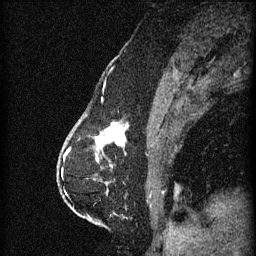
Breast MRI (dynamic contrast-enhanced), one sagittal slice; slice 23 of 60 in the series (ordered by position); 3 images stored at this slice position (order not interpretable as contrast timing); 1.5 T; TE 4.2 ms, TR 11 ms; 256 × 256 image matrix, field of view 180 × 180 mm. Patient: female, 63 years.
Outlined on this slice (semi-automatic segmentation, software-assisted and operator-edited):
- analysis volume of interest (the breast-tissue region the enhancement analysis was run in; not a lesion): bounding box (x1, y1, x2, y2) in pixels: (88, 120, 131, 153)
- tumour enhancement mask (voxels above the 70 % enhancement threshold inside the analysis volume of interest): (96, 124, 129, 151)